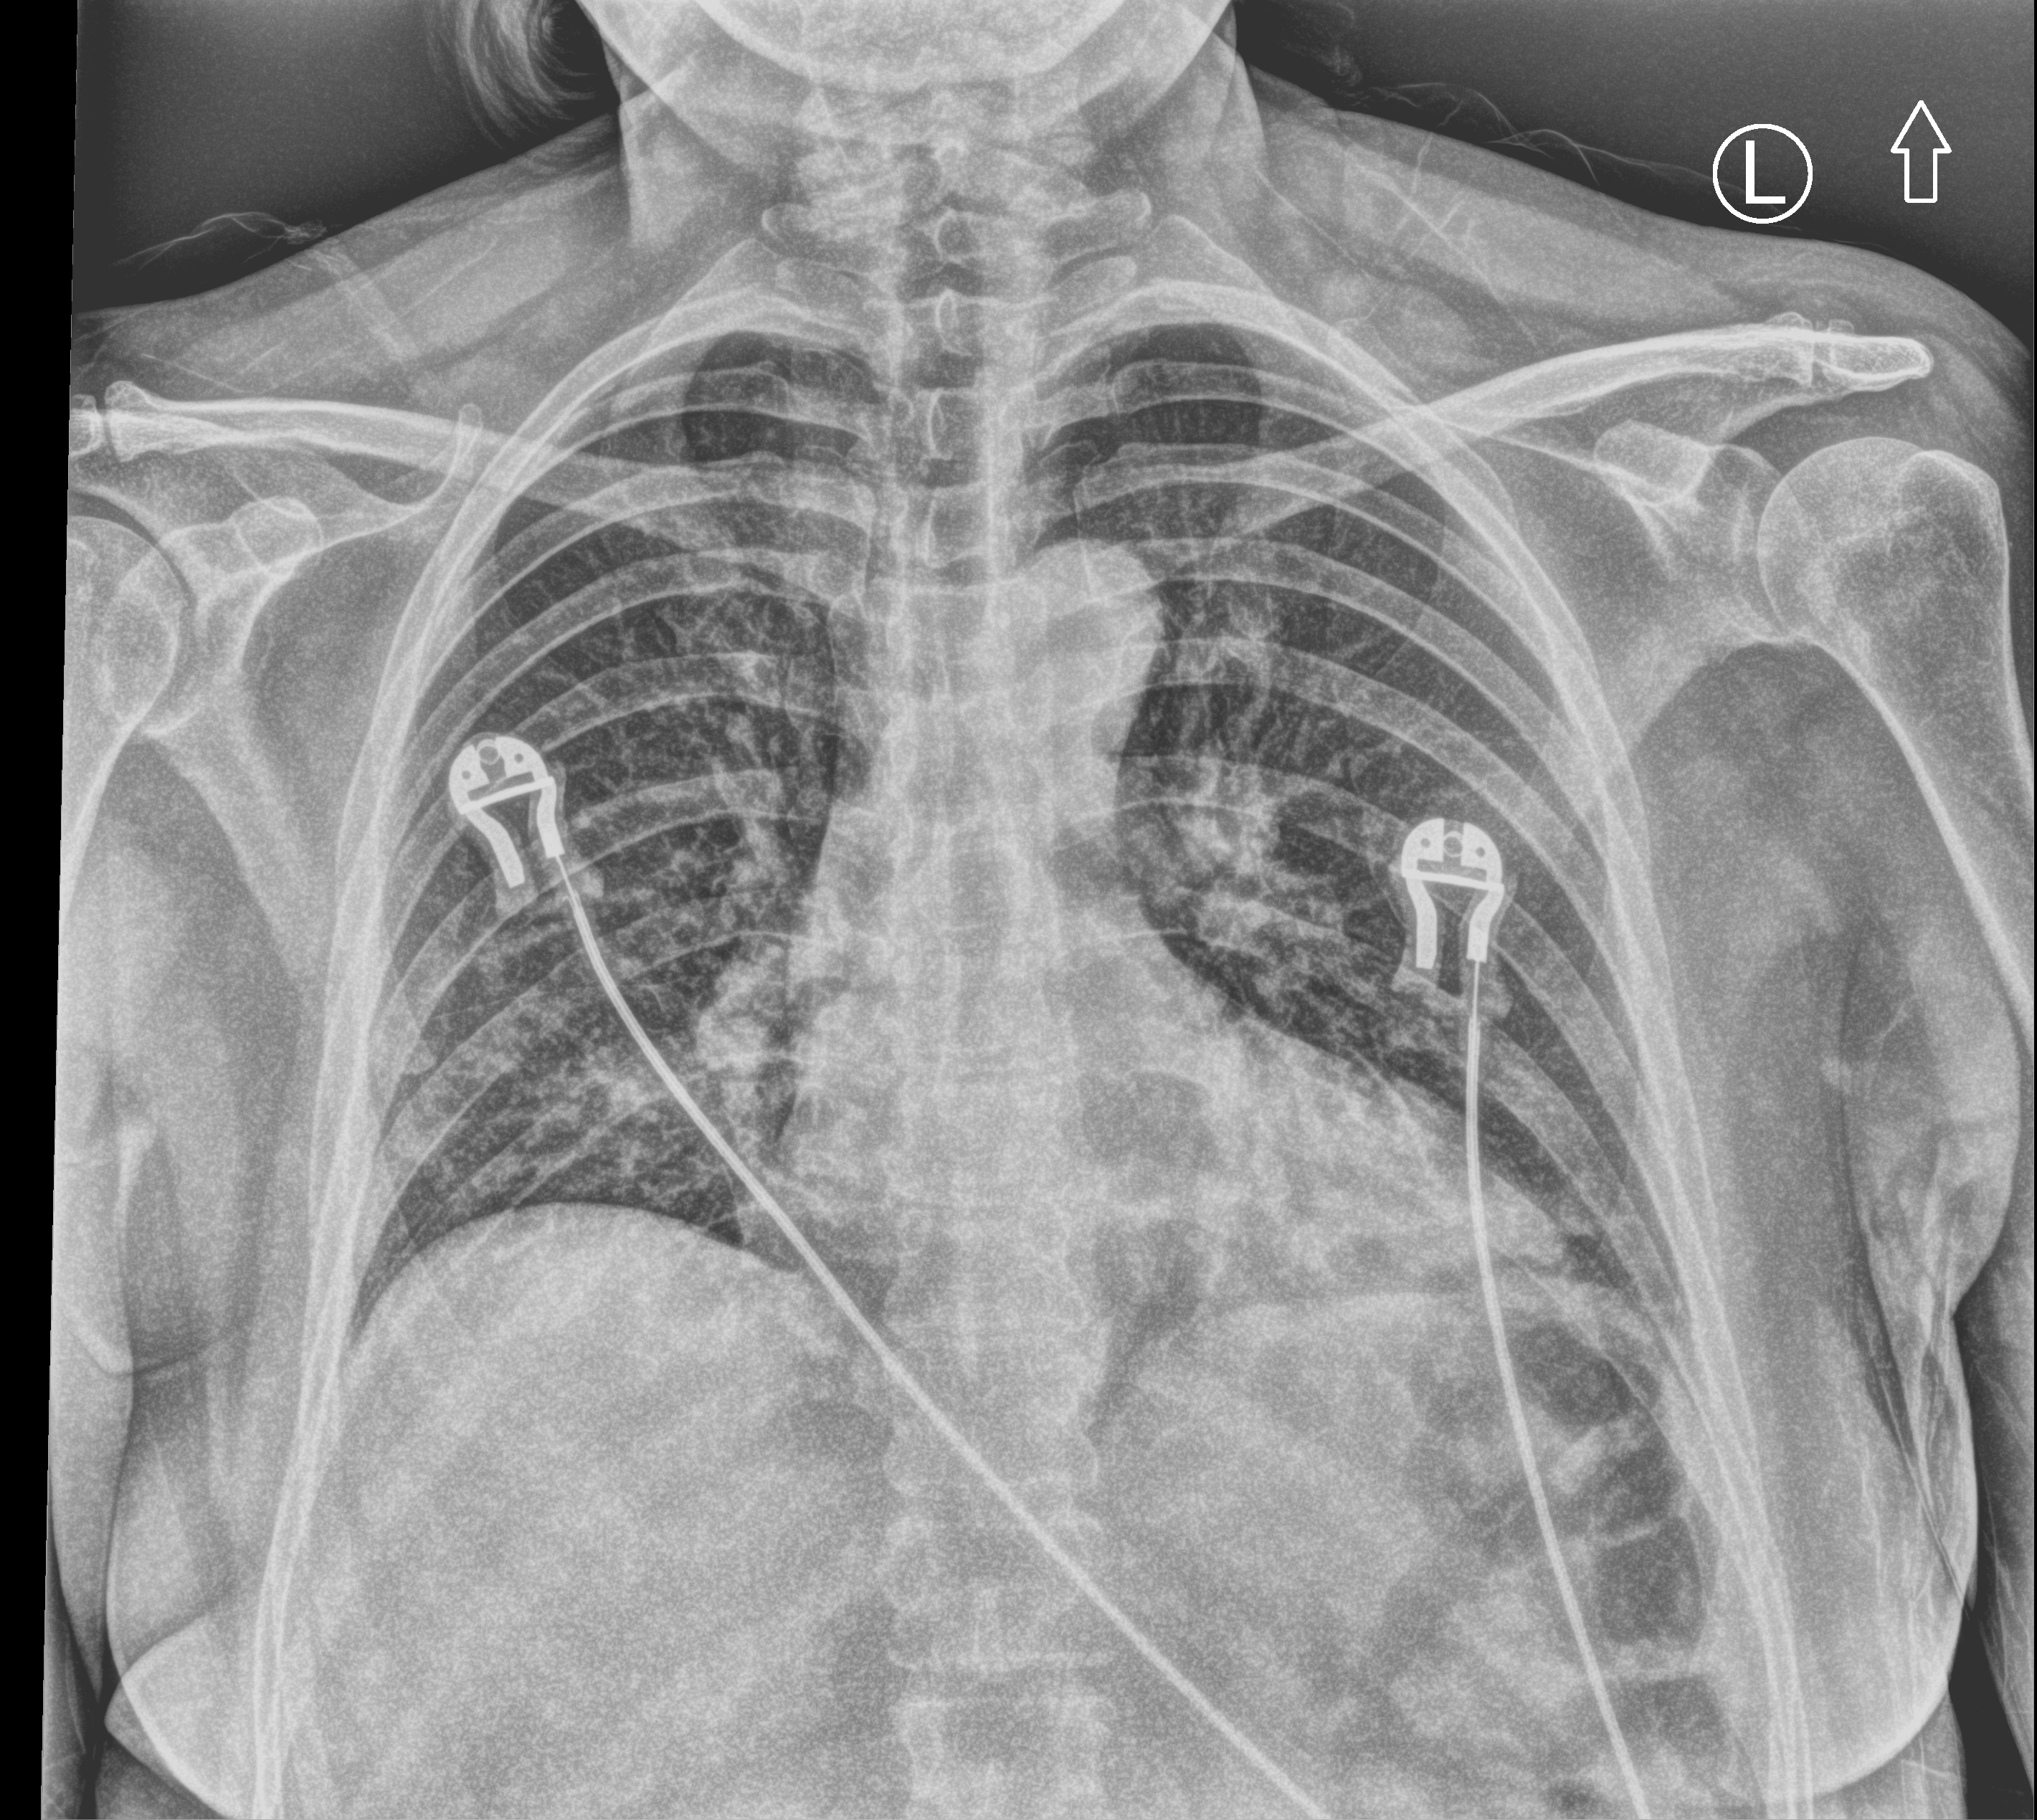
Portable chest radiograph, anteroposterior (AP) projection. Female patient hospitalised with COVID-19, age 18–59 years.
Hospital-stay facts (about this admission, not read from this image; timing relative to this image not recorded):
- smoking status (admission record): never
- mechanically ventilated during this hospital stay: no